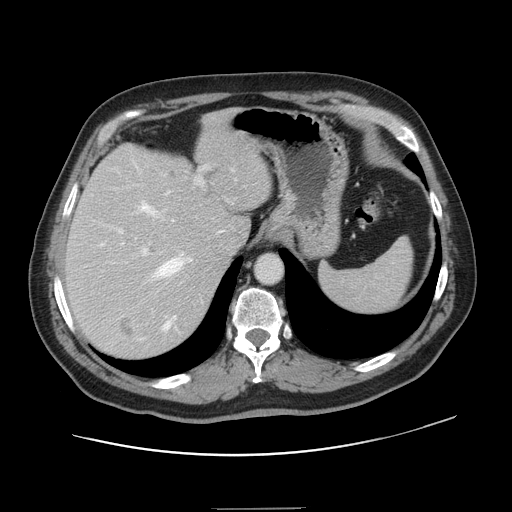
Contrast-enhanced abdominal CT, one axial slice. Slice 108 of 143 in the series (ordered by position). 120 kVp. Intravenous contrast given. Soft-tissue window (W 400 / L 40 HU). 2.5 mm slice thickness. 512 × 512 image matrix. Male patient, age 62 years. Case-level facts recorded for this patient, not image findings: diagnosis: colorectal cancer liver metastases, imaged before liver resection; multiple liver metastases: yes; largest metastasis: 2.7 cm; disease in both lobes: no.
Annotated regions visible in this slice (manually delineated by an expert):
- hepatic veins: bounding box [x1, y1, x2, y2] px = [101, 169, 236, 330]
- liver: [67, 115, 271, 359]
- planned liver remnant (the part of the liver to remain after resection): [66, 116, 271, 274]
- portal vein (with intrahepatic branches): [119, 165, 209, 276]
- liver metastasis: [119, 319, 135, 339]
- liver metastasis: [168, 169, 180, 182]